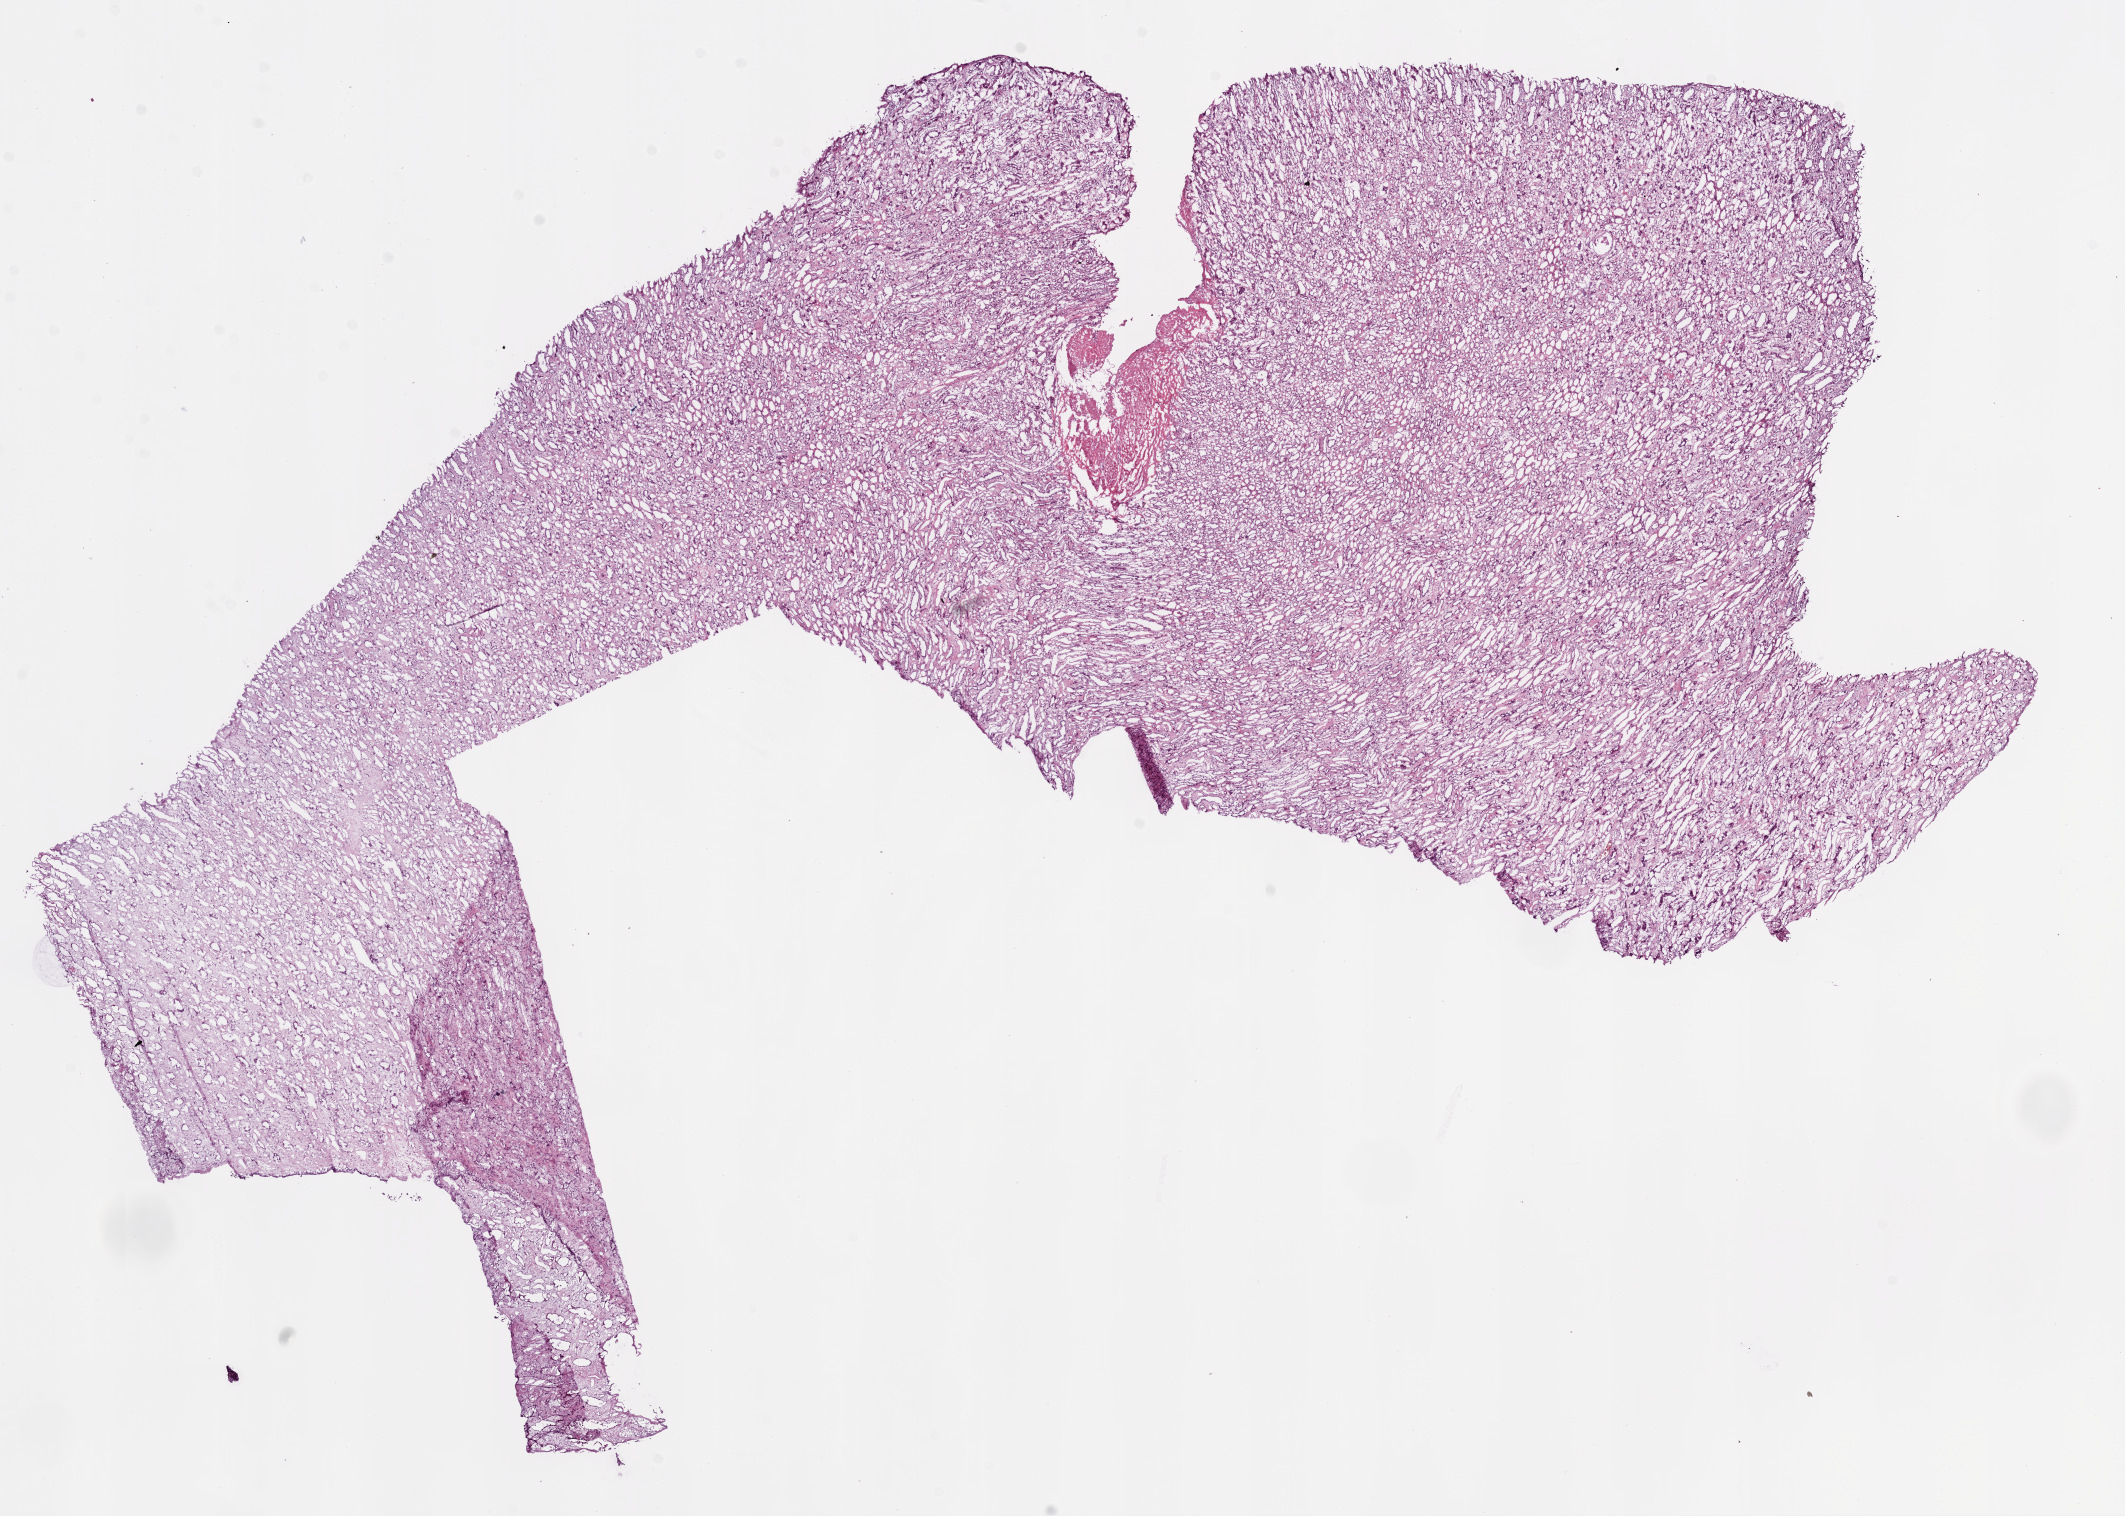
H&E-stained whole-slide image, low-resolution overview of the scanned area, about 17.1 x 12.2 mm (slide scanned at 20x); frozen section from the bottom of the tissue portion; solid tissue normal (non-tumour tissue) sample from the kidney. Female, age 79 years at initial diagnosis.
This section: solid tissue normal (non-tumour) sample from the same patient. Patient diagnosis: Clear cell adenocarcinoma, NOS.